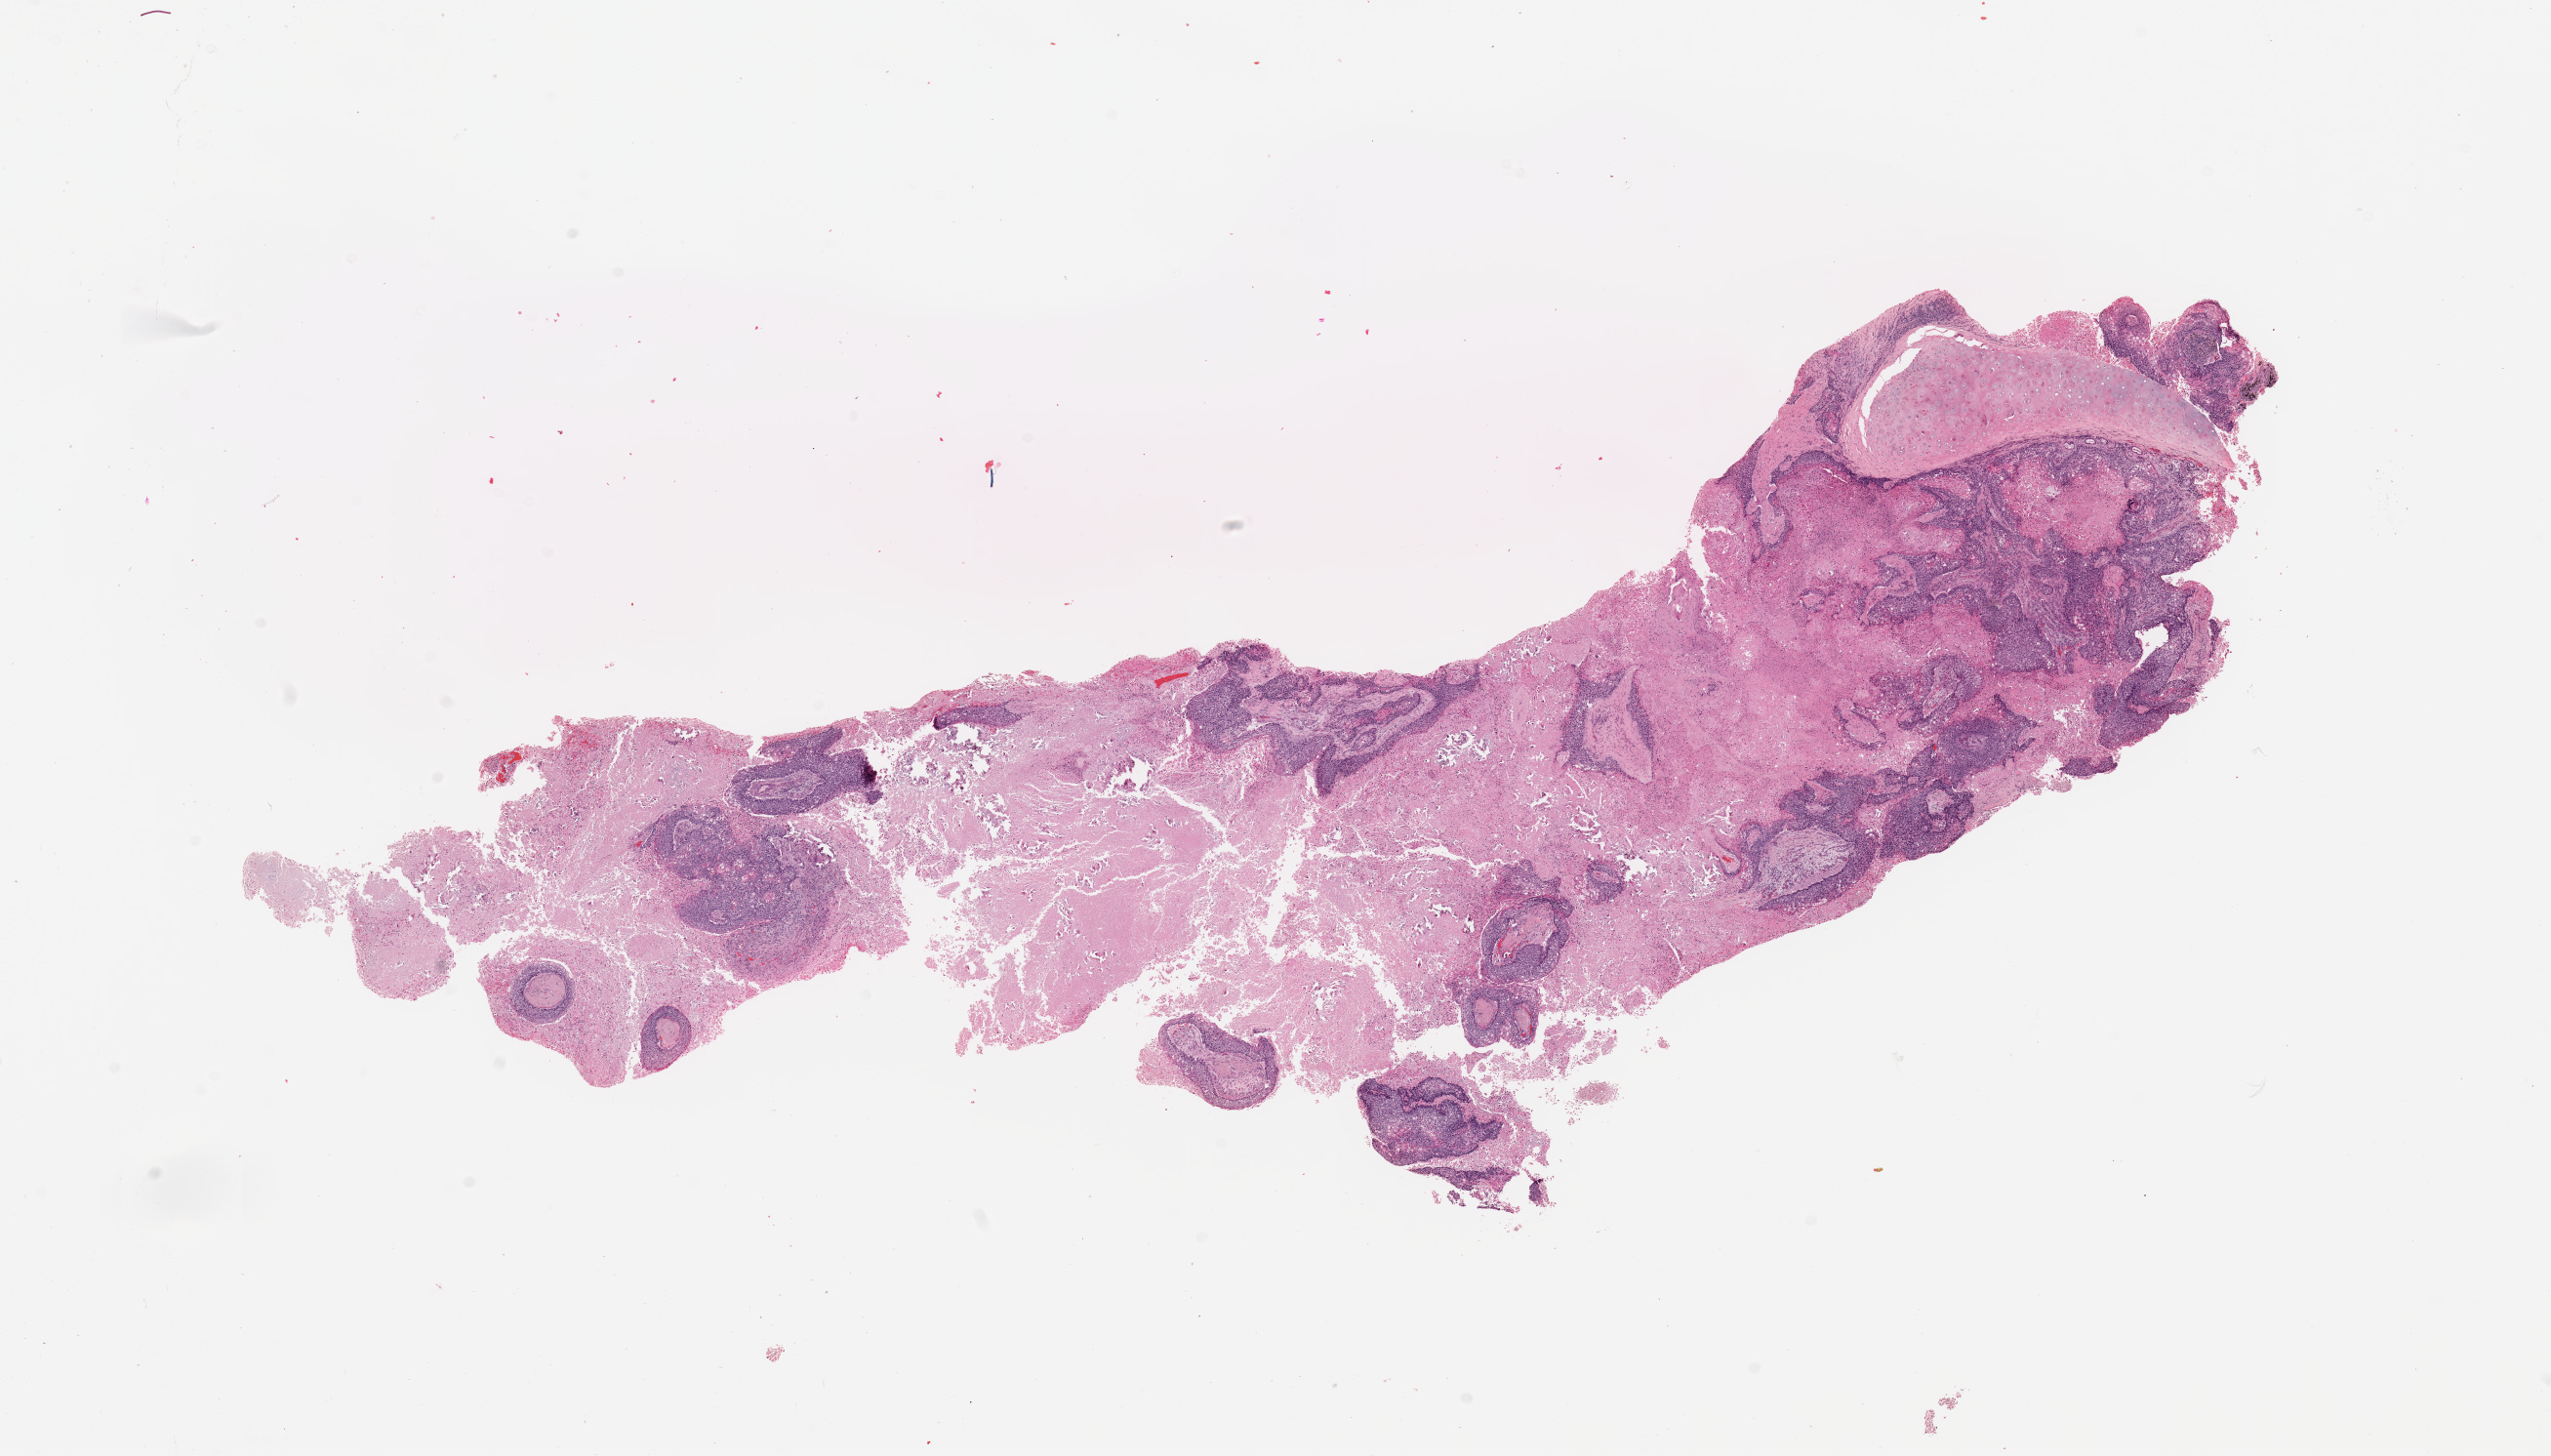
Digitized H&E-stained tissue section (whole slide) — low-resolution overview of the scanned area, about 20.7 x 11.8 mm (slide scanned at 20x), tumour tissue sample, lung. Patient: male, age 78 years. Histologic grade: G2 (moderately differentiated).
* diagnosis: Squamous cell carcinoma, NOS
* AJCC pathologic stage: III
* primary tumour site (as recorded): right middle lobe